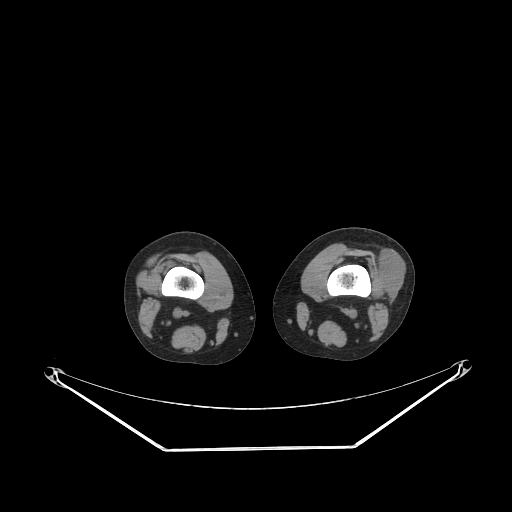
CT of an extremity soft-tissue mass (from a PET/CT study), one axial slice; position 174 of 223 along the scan axis; reconstruction kernel STANDARD; 140 kVp; soft-tissue window (W 400 / L 40 HU); 512 × 512 image matrix. Female patient. From the clinical record (not read from this slice): histological type: spindle cell suggestive of biphasic synovial sarcoma; grade: intermediate; site of the primary tumour: left knee.
Annotated regions visible in this slice (expert contour drawn on MRI and transferred to this co-registered scan by the dataset authors):
- gross tumour volume including surrounding oedema: bounding box [x1, y1, x2, y2] px = [372, 247, 403, 298]
- gross tumour volume (mass): [374, 249, 403, 298]